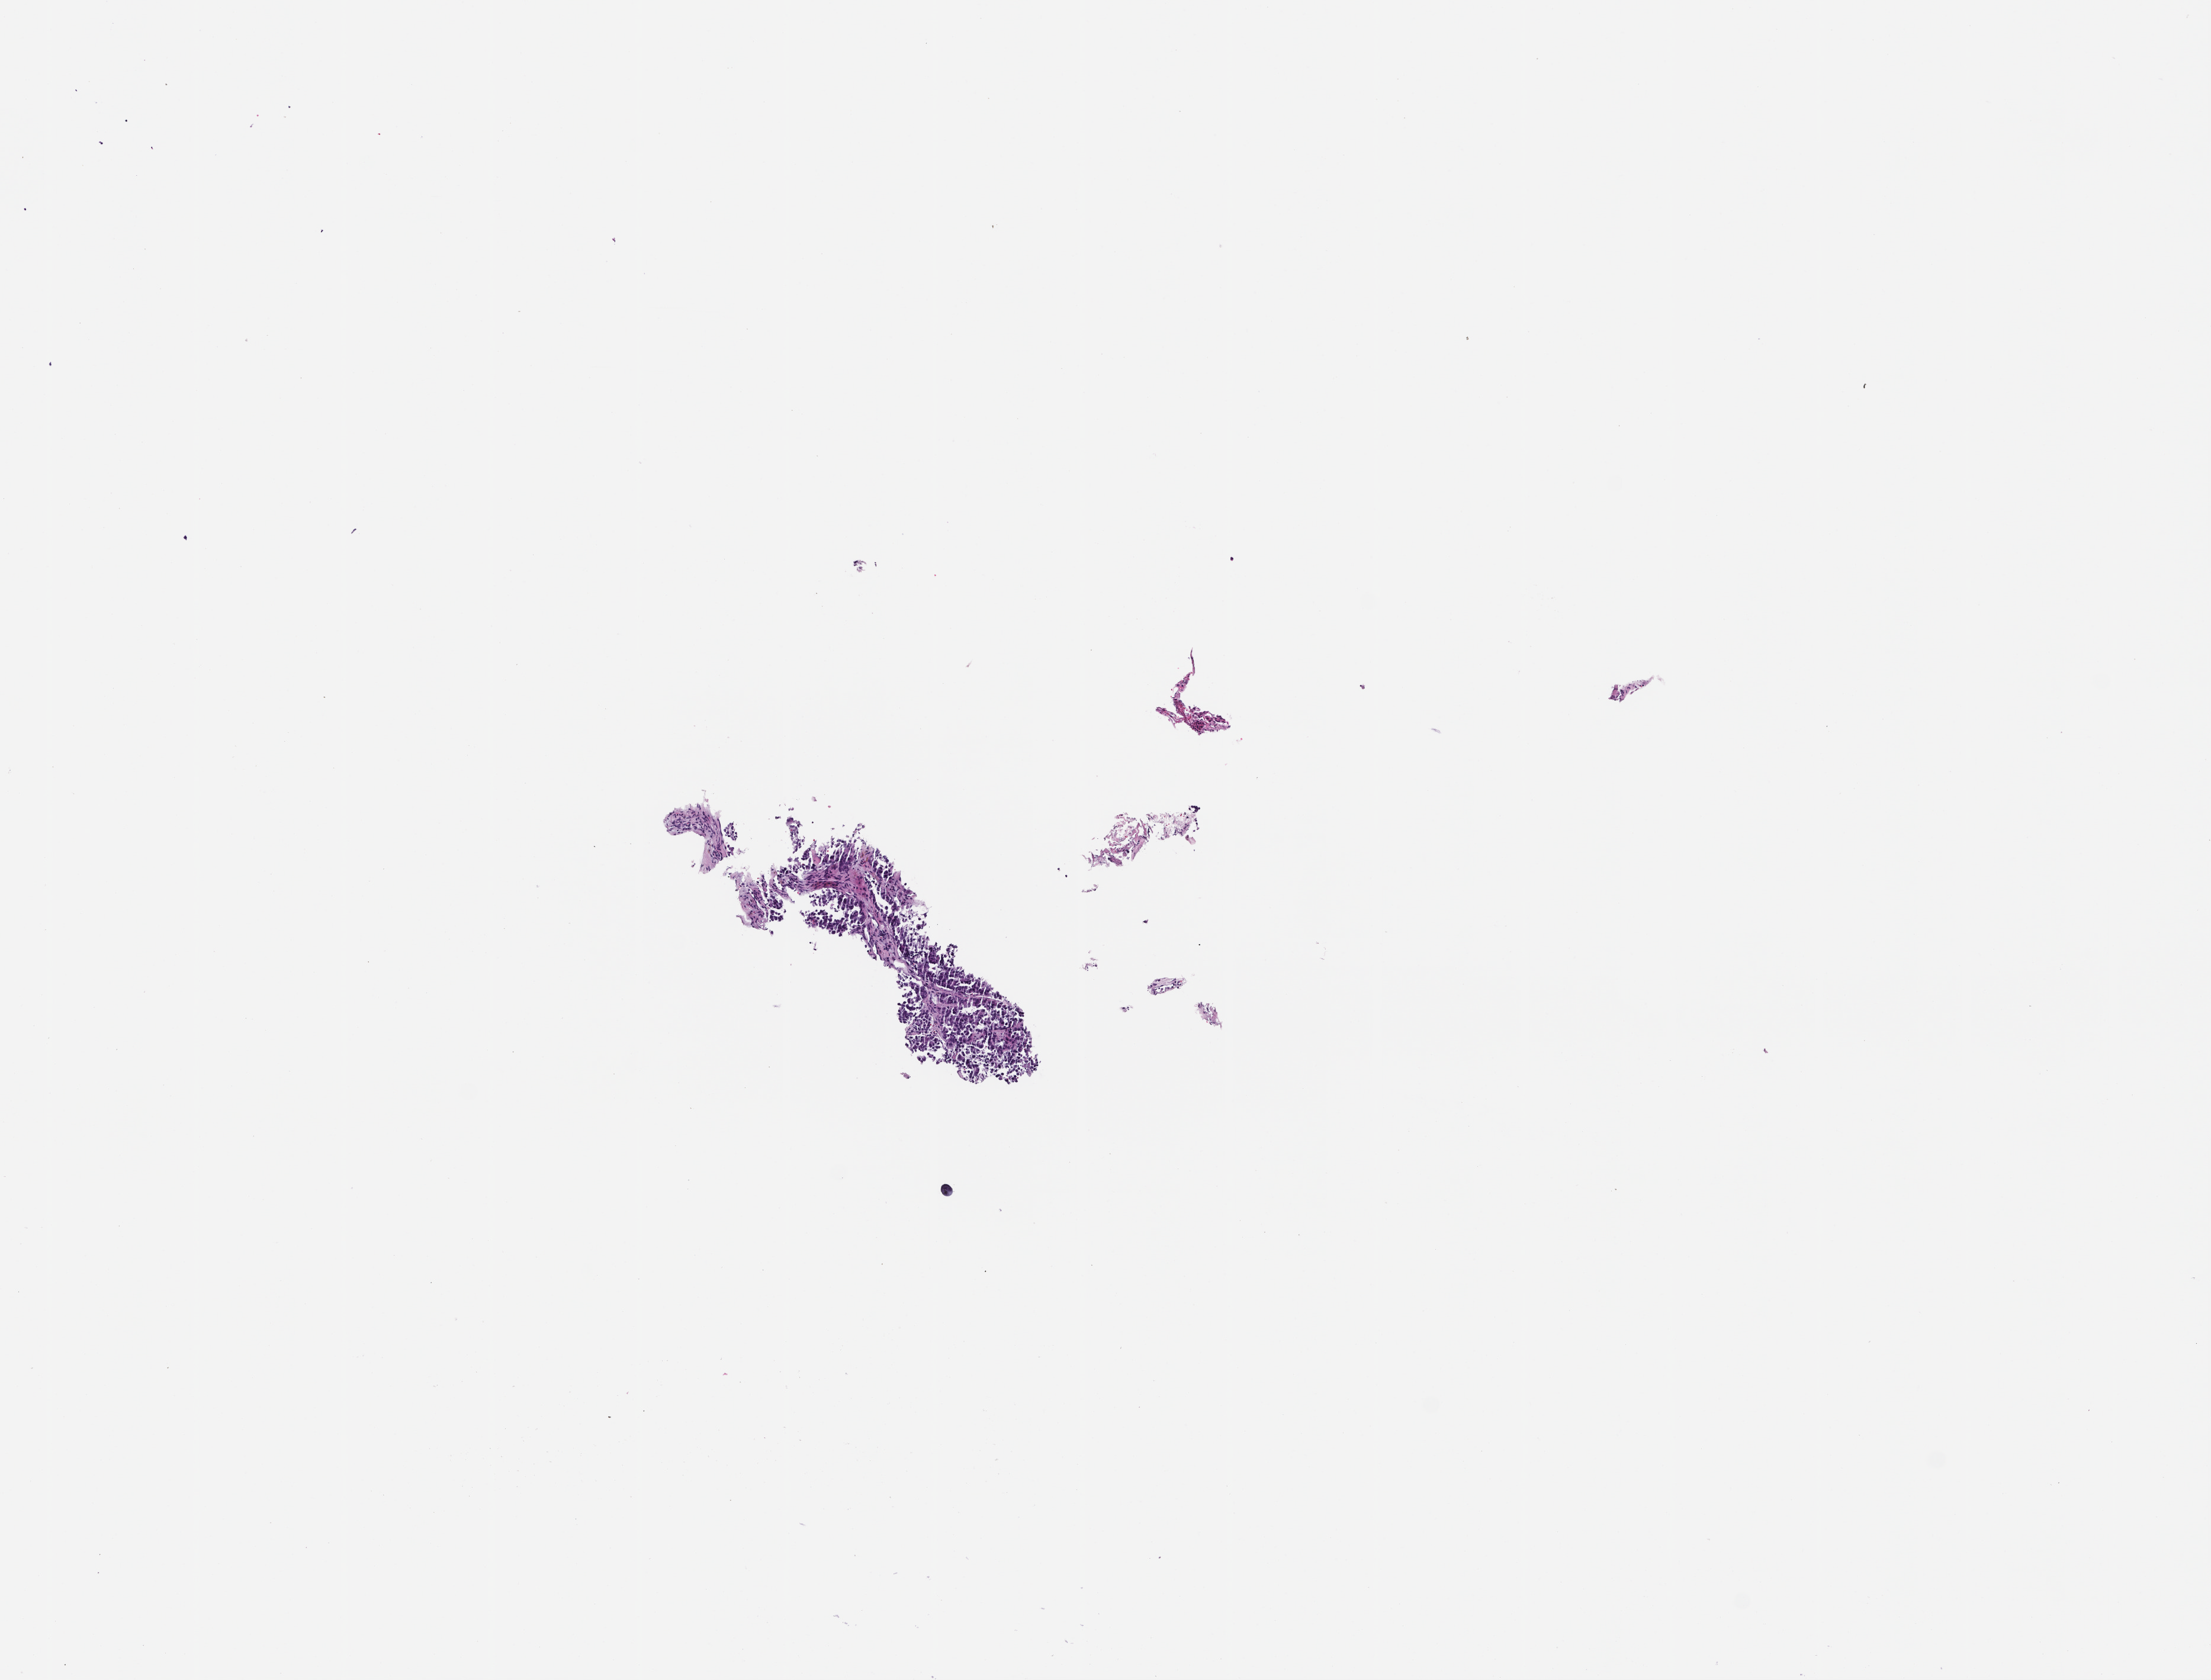
Whole-slide image, hematoxylin and eosin (H&E) stain — low-resolution overview of the scanned area, about 7.5 x 5.7 mm; formalin-fixed, paraffin-embedded (FFPE) tissue. Male patient.
This section: metastatic tumor tissue. Patient diagnosis (primary): Non-Small Cell Lung Carcinoma.